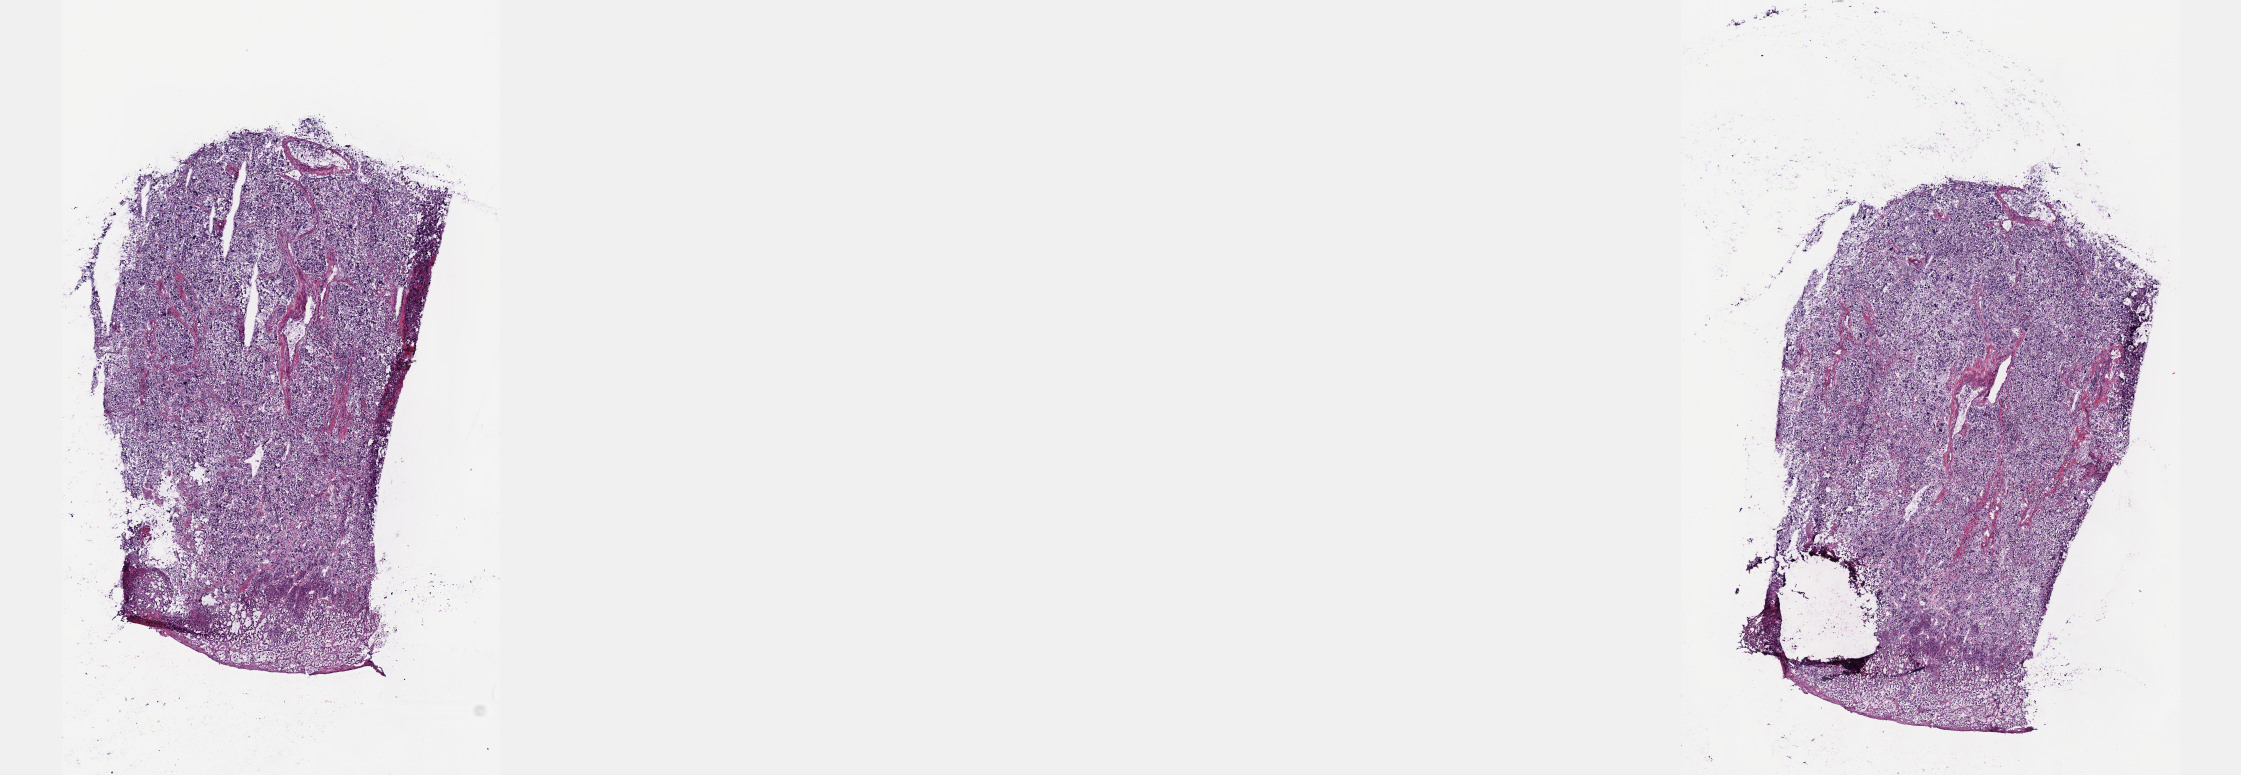
H&E whole-slide image — shown as a low-resolution overview of the whole scanned area (about 18.1 x 6.3 mm). Frozen section from the top of the tissue portion. Sample: primary tumour, adrenal gland. Male patient; age at initial diagnosis 45 years. Pathologist review of this section (percent, as recorded): tumour cells 100%, tumour nuclei 80%.
Diagnosis: Pheochromocytoma, NOS.